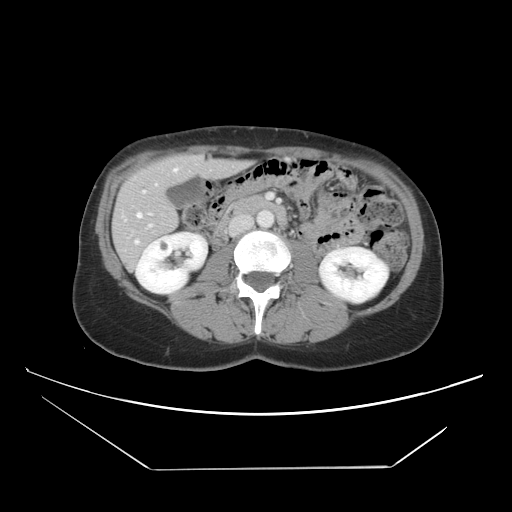
Contrast-enhanced abdominal CT, one axial slice. Slice 17 of 42 in the series (ordered by position). 120 kVp. Intravenous contrast given. Soft-tissue window (W 400 / L 40 HU). 5 mm slice thickness. 512 × 512 image matrix, field of view 399 × 399 mm. Female patient, age 52 years. From the clinical record (not read from this slice): diagnosis: colorectal cancer liver metastases, imaged before liver resection; multiple liver metastases: yes; largest metastasis: 5.5 cm.
Annotated regions visible in this slice (outlined manually by an expert reader):
- hepatic veins: box from (x=121, y=164) to (x=198, y=244) px
- liver: (x=114, y=156)–(x=245, y=267)
- planned liver remnant (the part of the liver to remain after resection): (x=119, y=156)–(x=214, y=213)
- portal vein (with intrahepatic branches): (x=142, y=190)–(x=270, y=228)